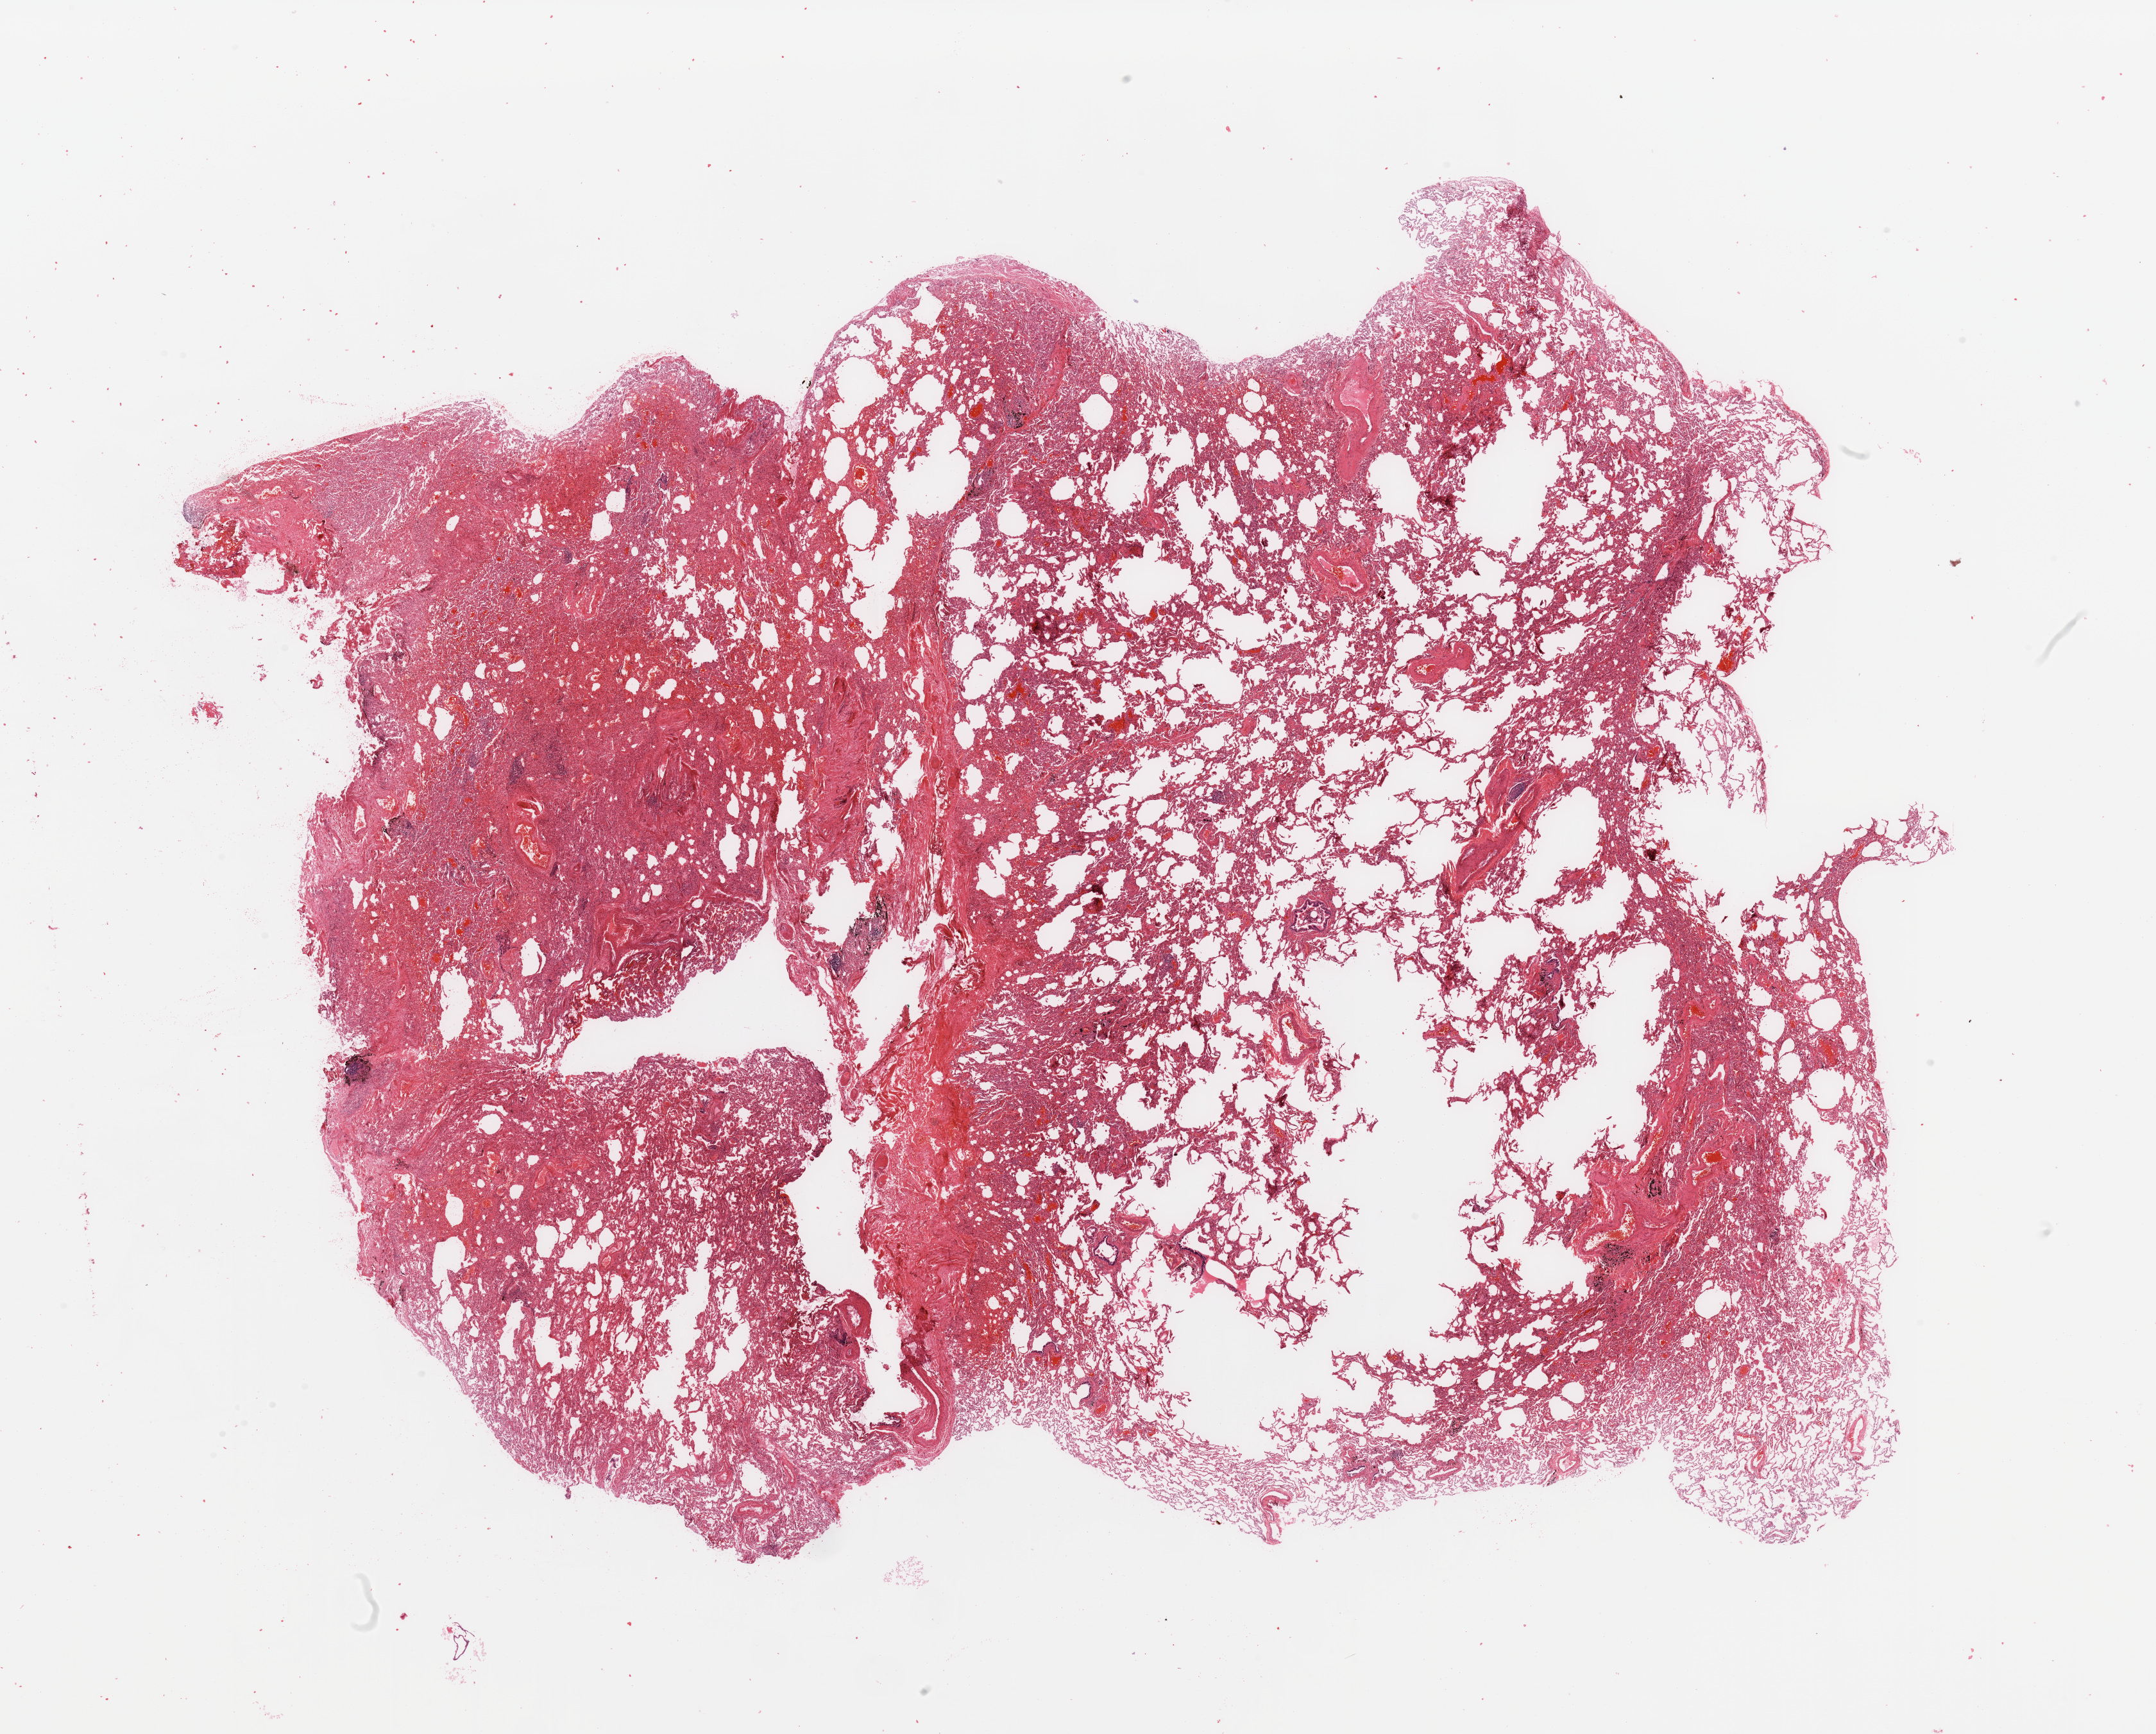
Digitized Hematoxylin and eosin (H&E) stained tissue section (whole slide) — low-resolution overview of the scanned area, about 26.6 x 21.4 mm (slide scanned at 20x). Normal (non-tumour) tissue sample, sampled site: lung. Patient: female, age 72 years.
This section: normal (non-tumour) tissue from the same patient. Patient diagnosis: Adenocarcinoma, NOS.